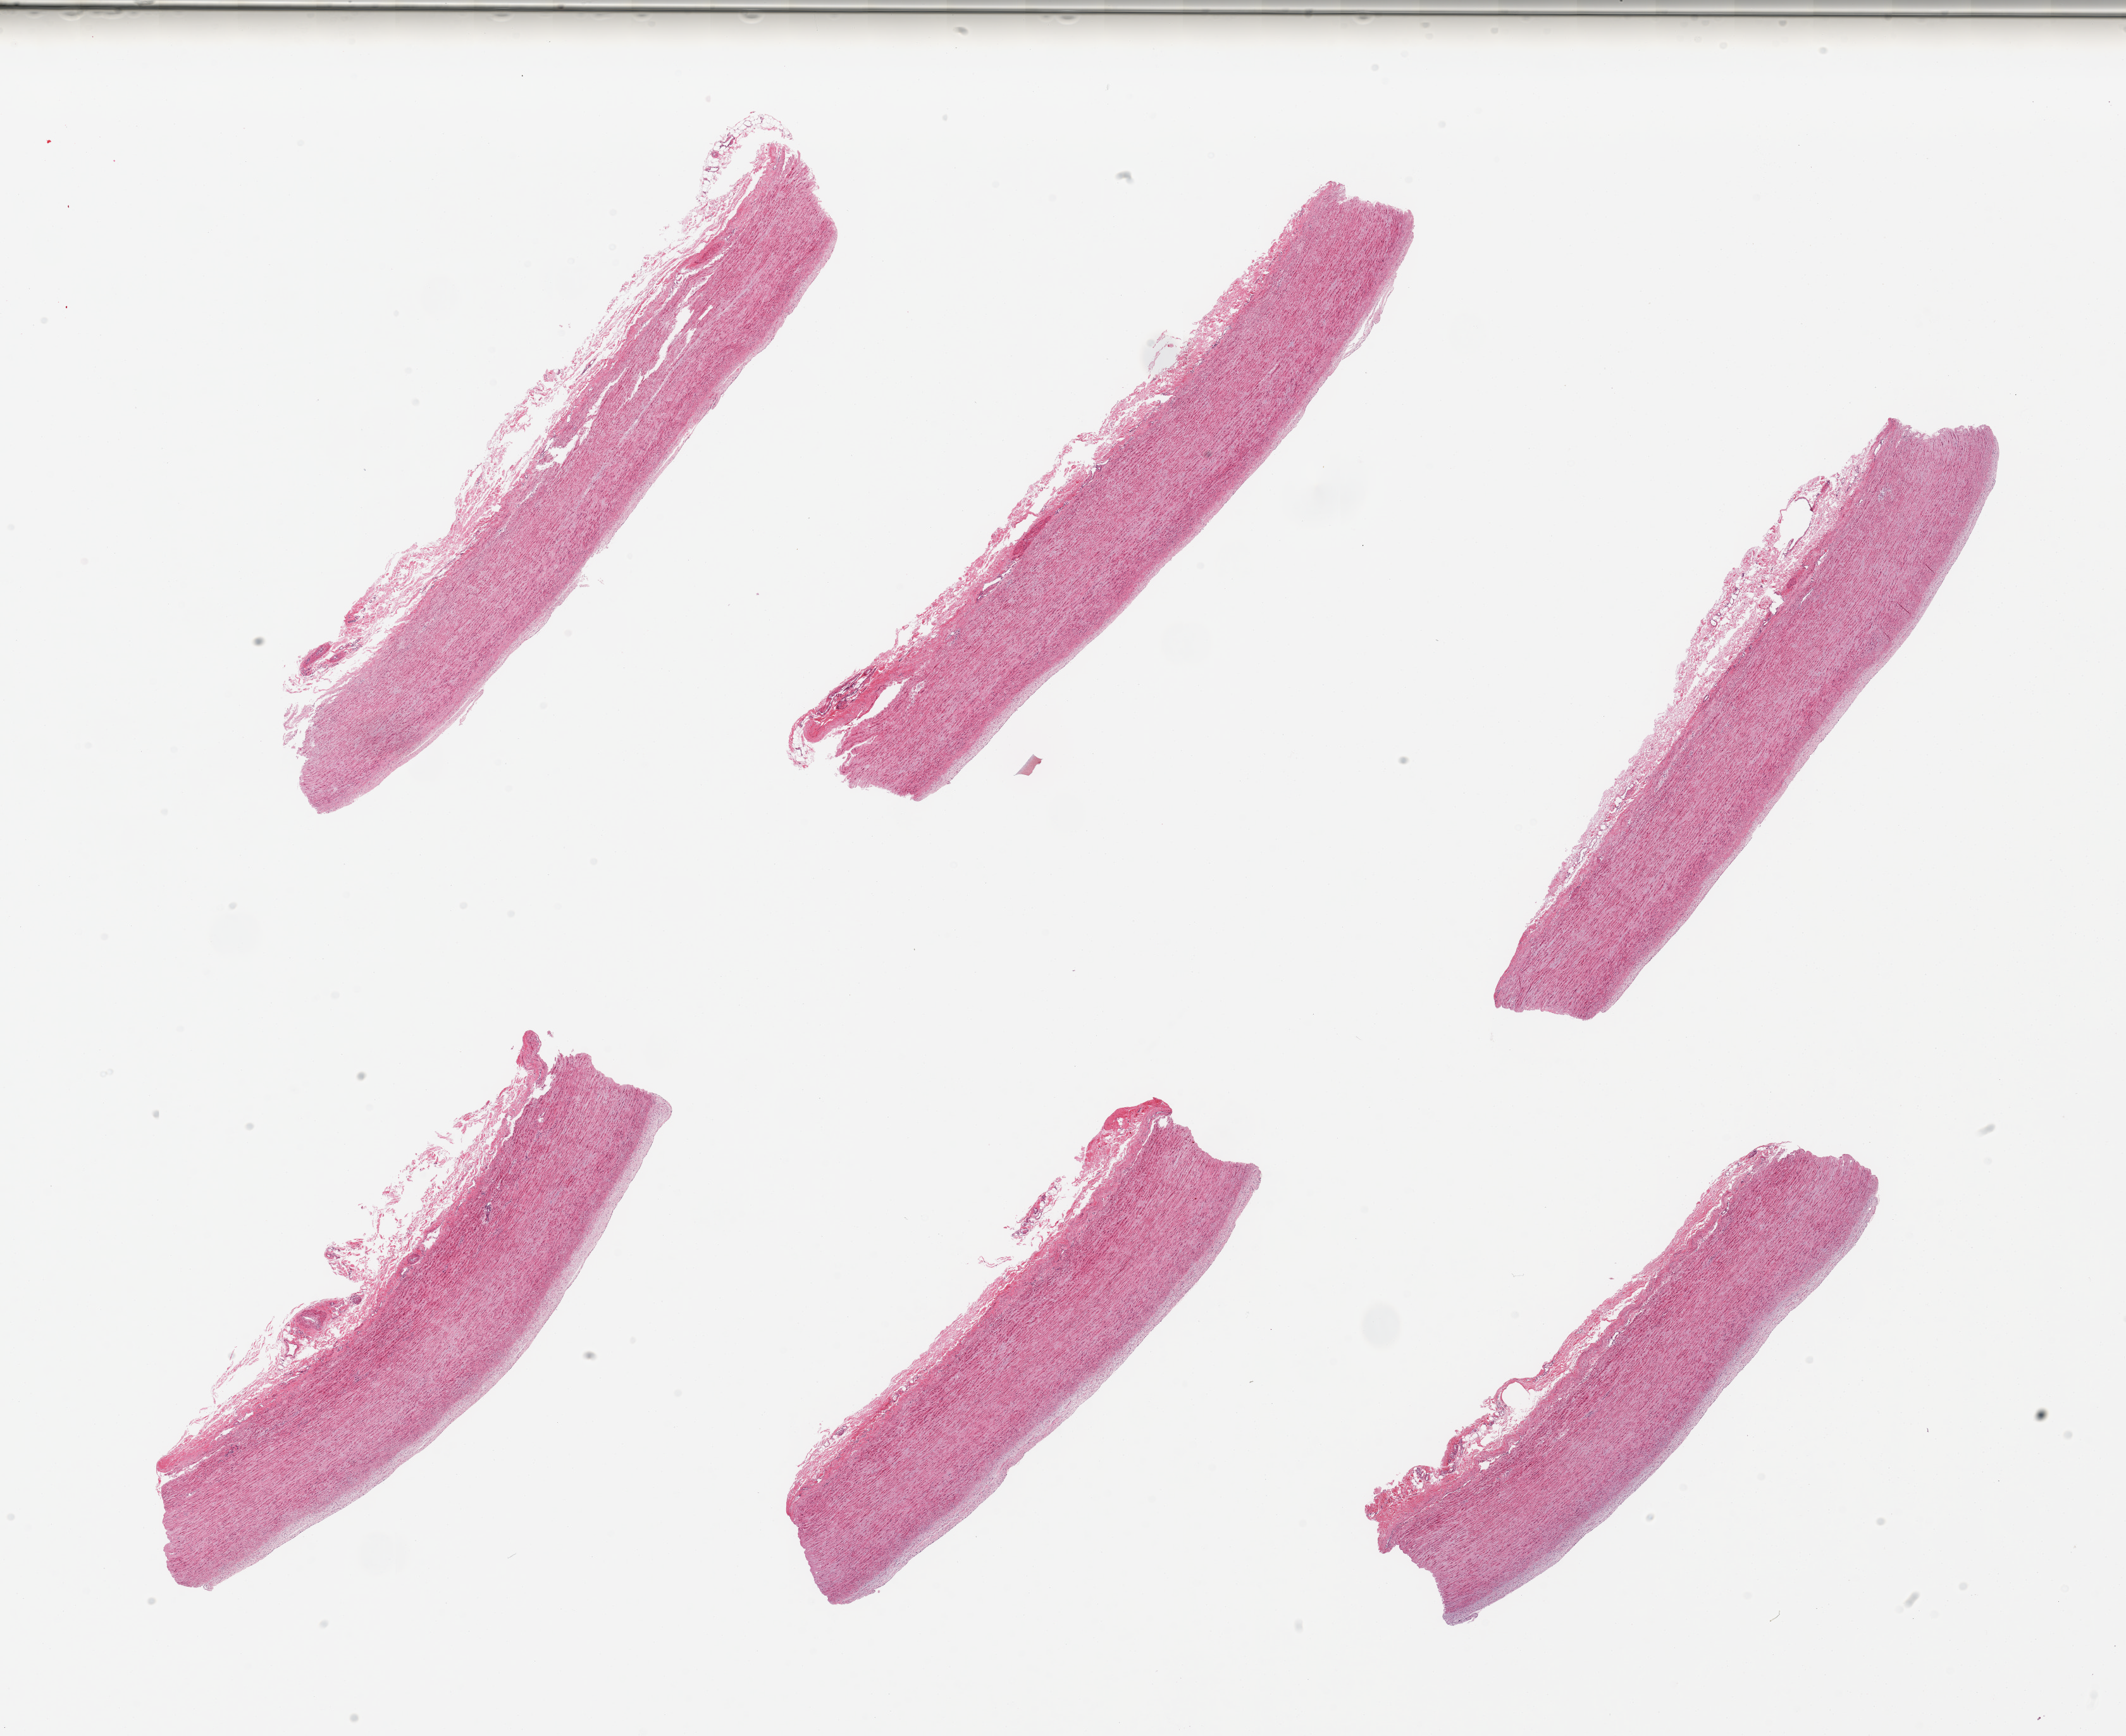
Whole-slide image, hematoxylin and eosin (H&E) stain, whole scanned area (about 26.6 x 21.7 mm, slide scanned at 20x) shown as a low-resolution overview, PAXgene-fixed, paraffin-embedded tissue, sampled site (target tissue): aorta, tissue donor sample. Male donor.
• pathologist's review note for this sample: 6 pieces, atherosis up to ~0.2mm